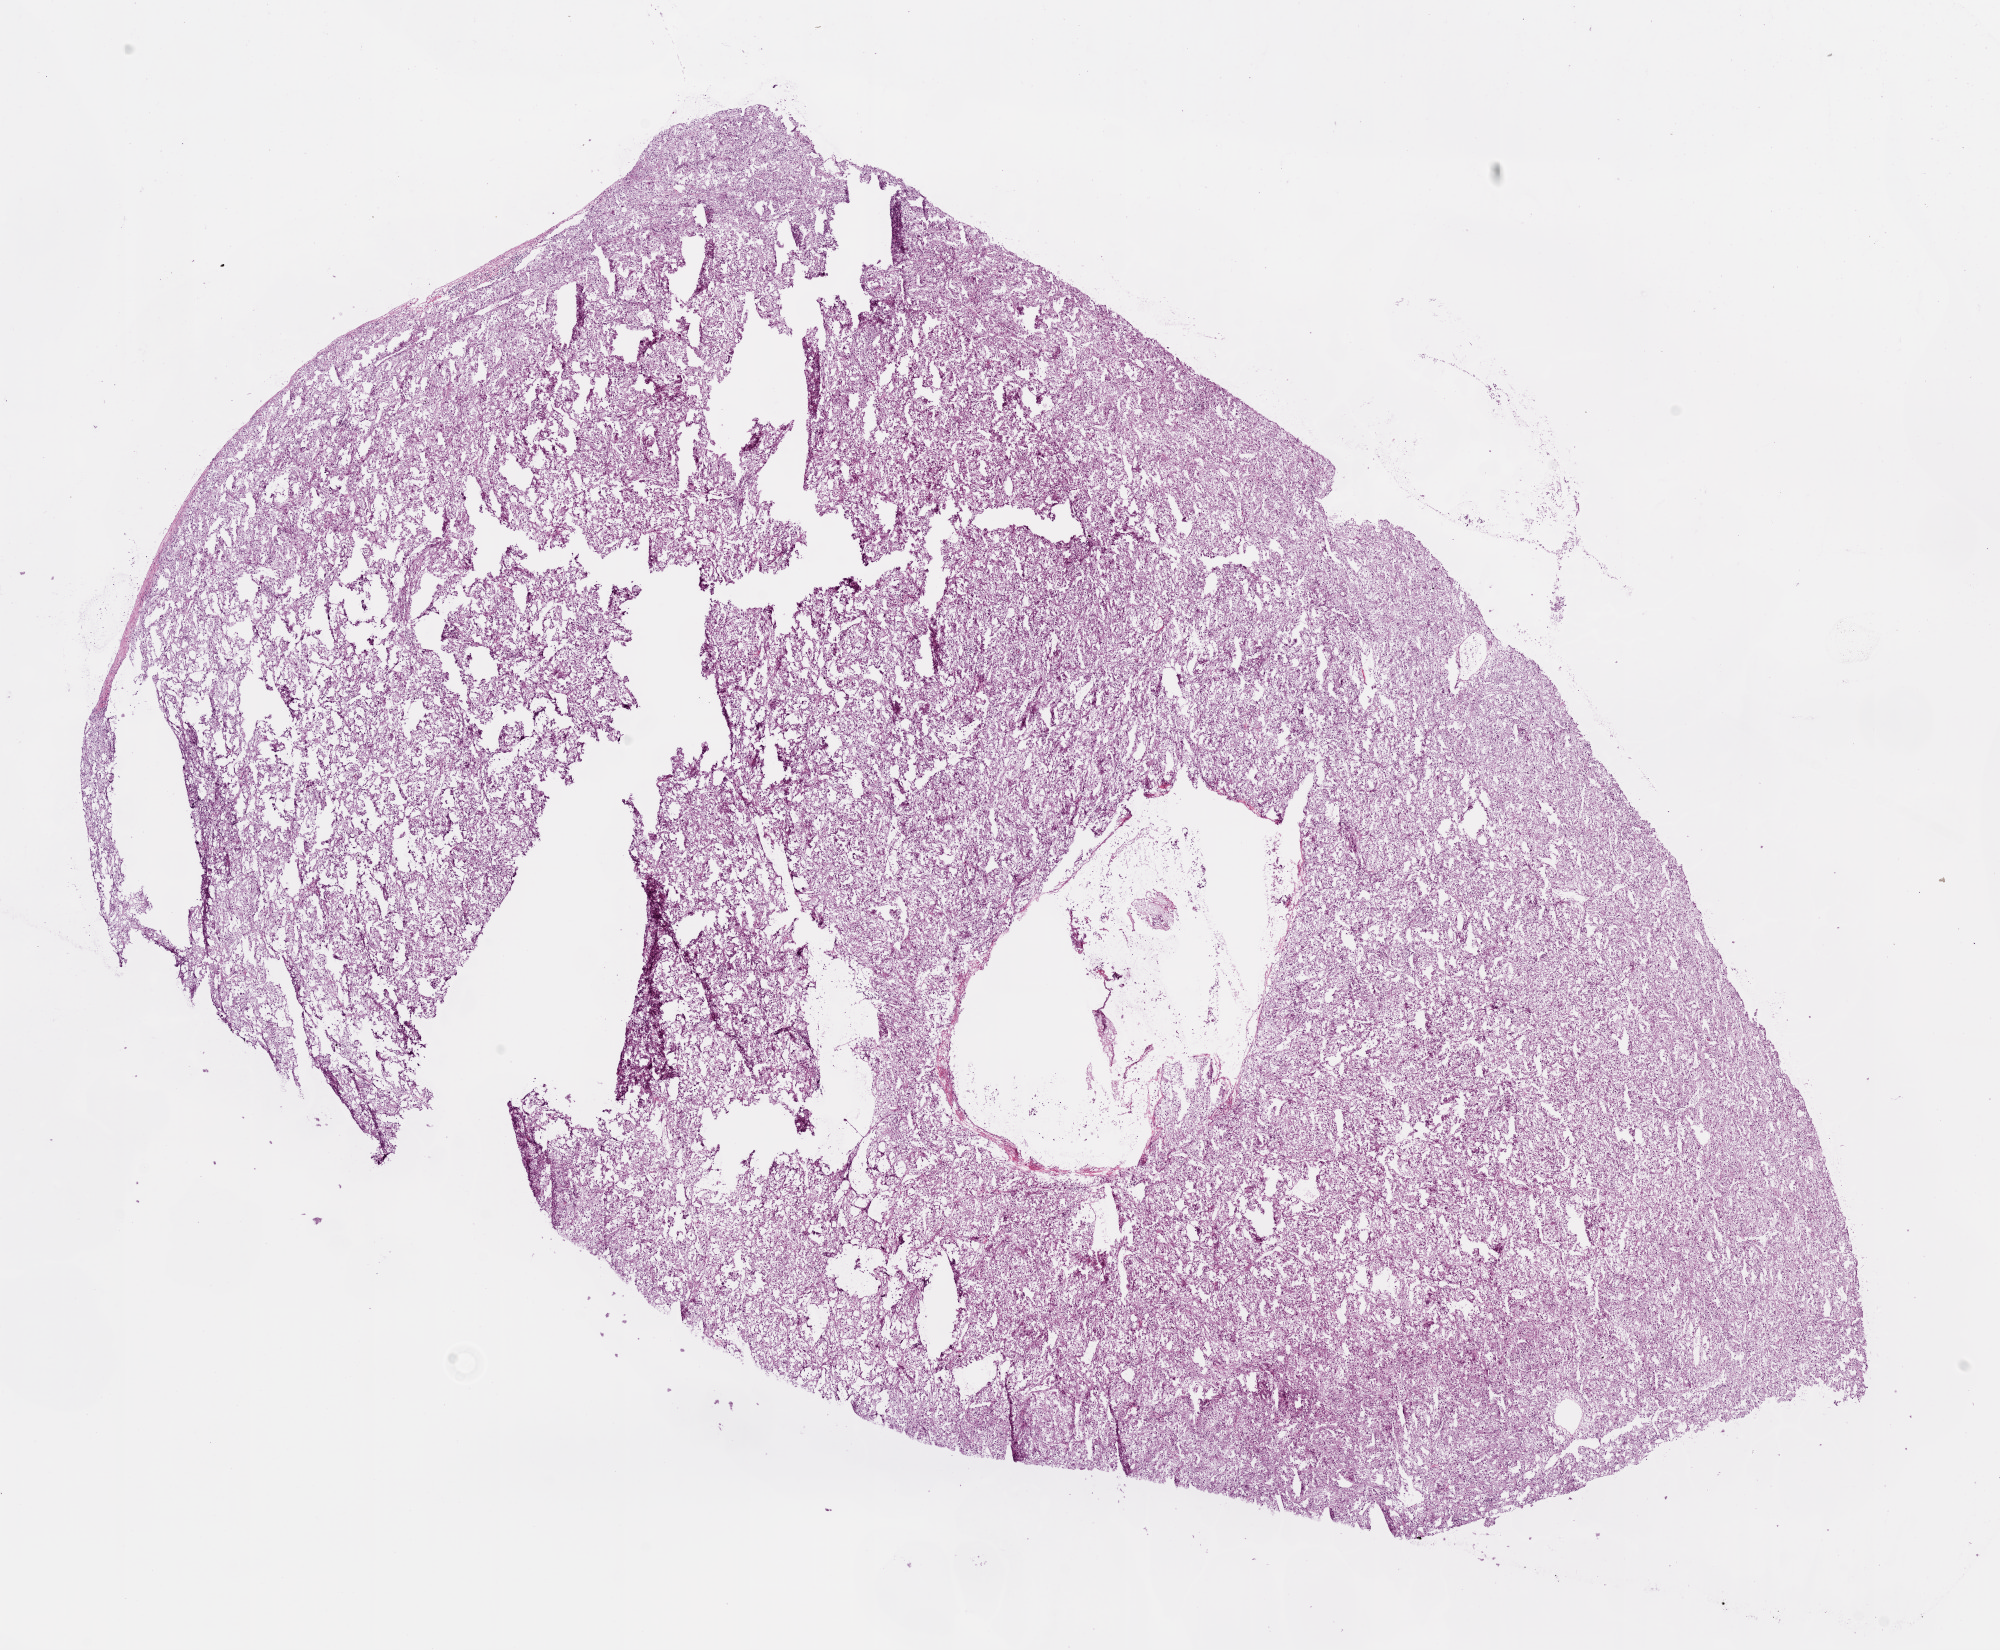
H&E whole-slide image — a low-resolution overview of the entire scanned area, about 16.0 x 13.2 mm (slide scanned at 20x); frozen section; sample: primary tumour, kidney. Patient: male, age at initial diagnosis 65 years. Histologic grade: G4 (undifferentiated). Pathologist review of this section (percent, as recorded): tumour cells 95%, tumour nuclei 85%, normal cells 0%, stromal cells 5%, necrosis 0%.
* TNM: T3b N0 M0
* AJCC pathologic stage: III (6th edition)
* diagnosis: Clear cell adenocarcinoma, NOS
* lymph nodes positive (case pathology): 0 of 4 examined